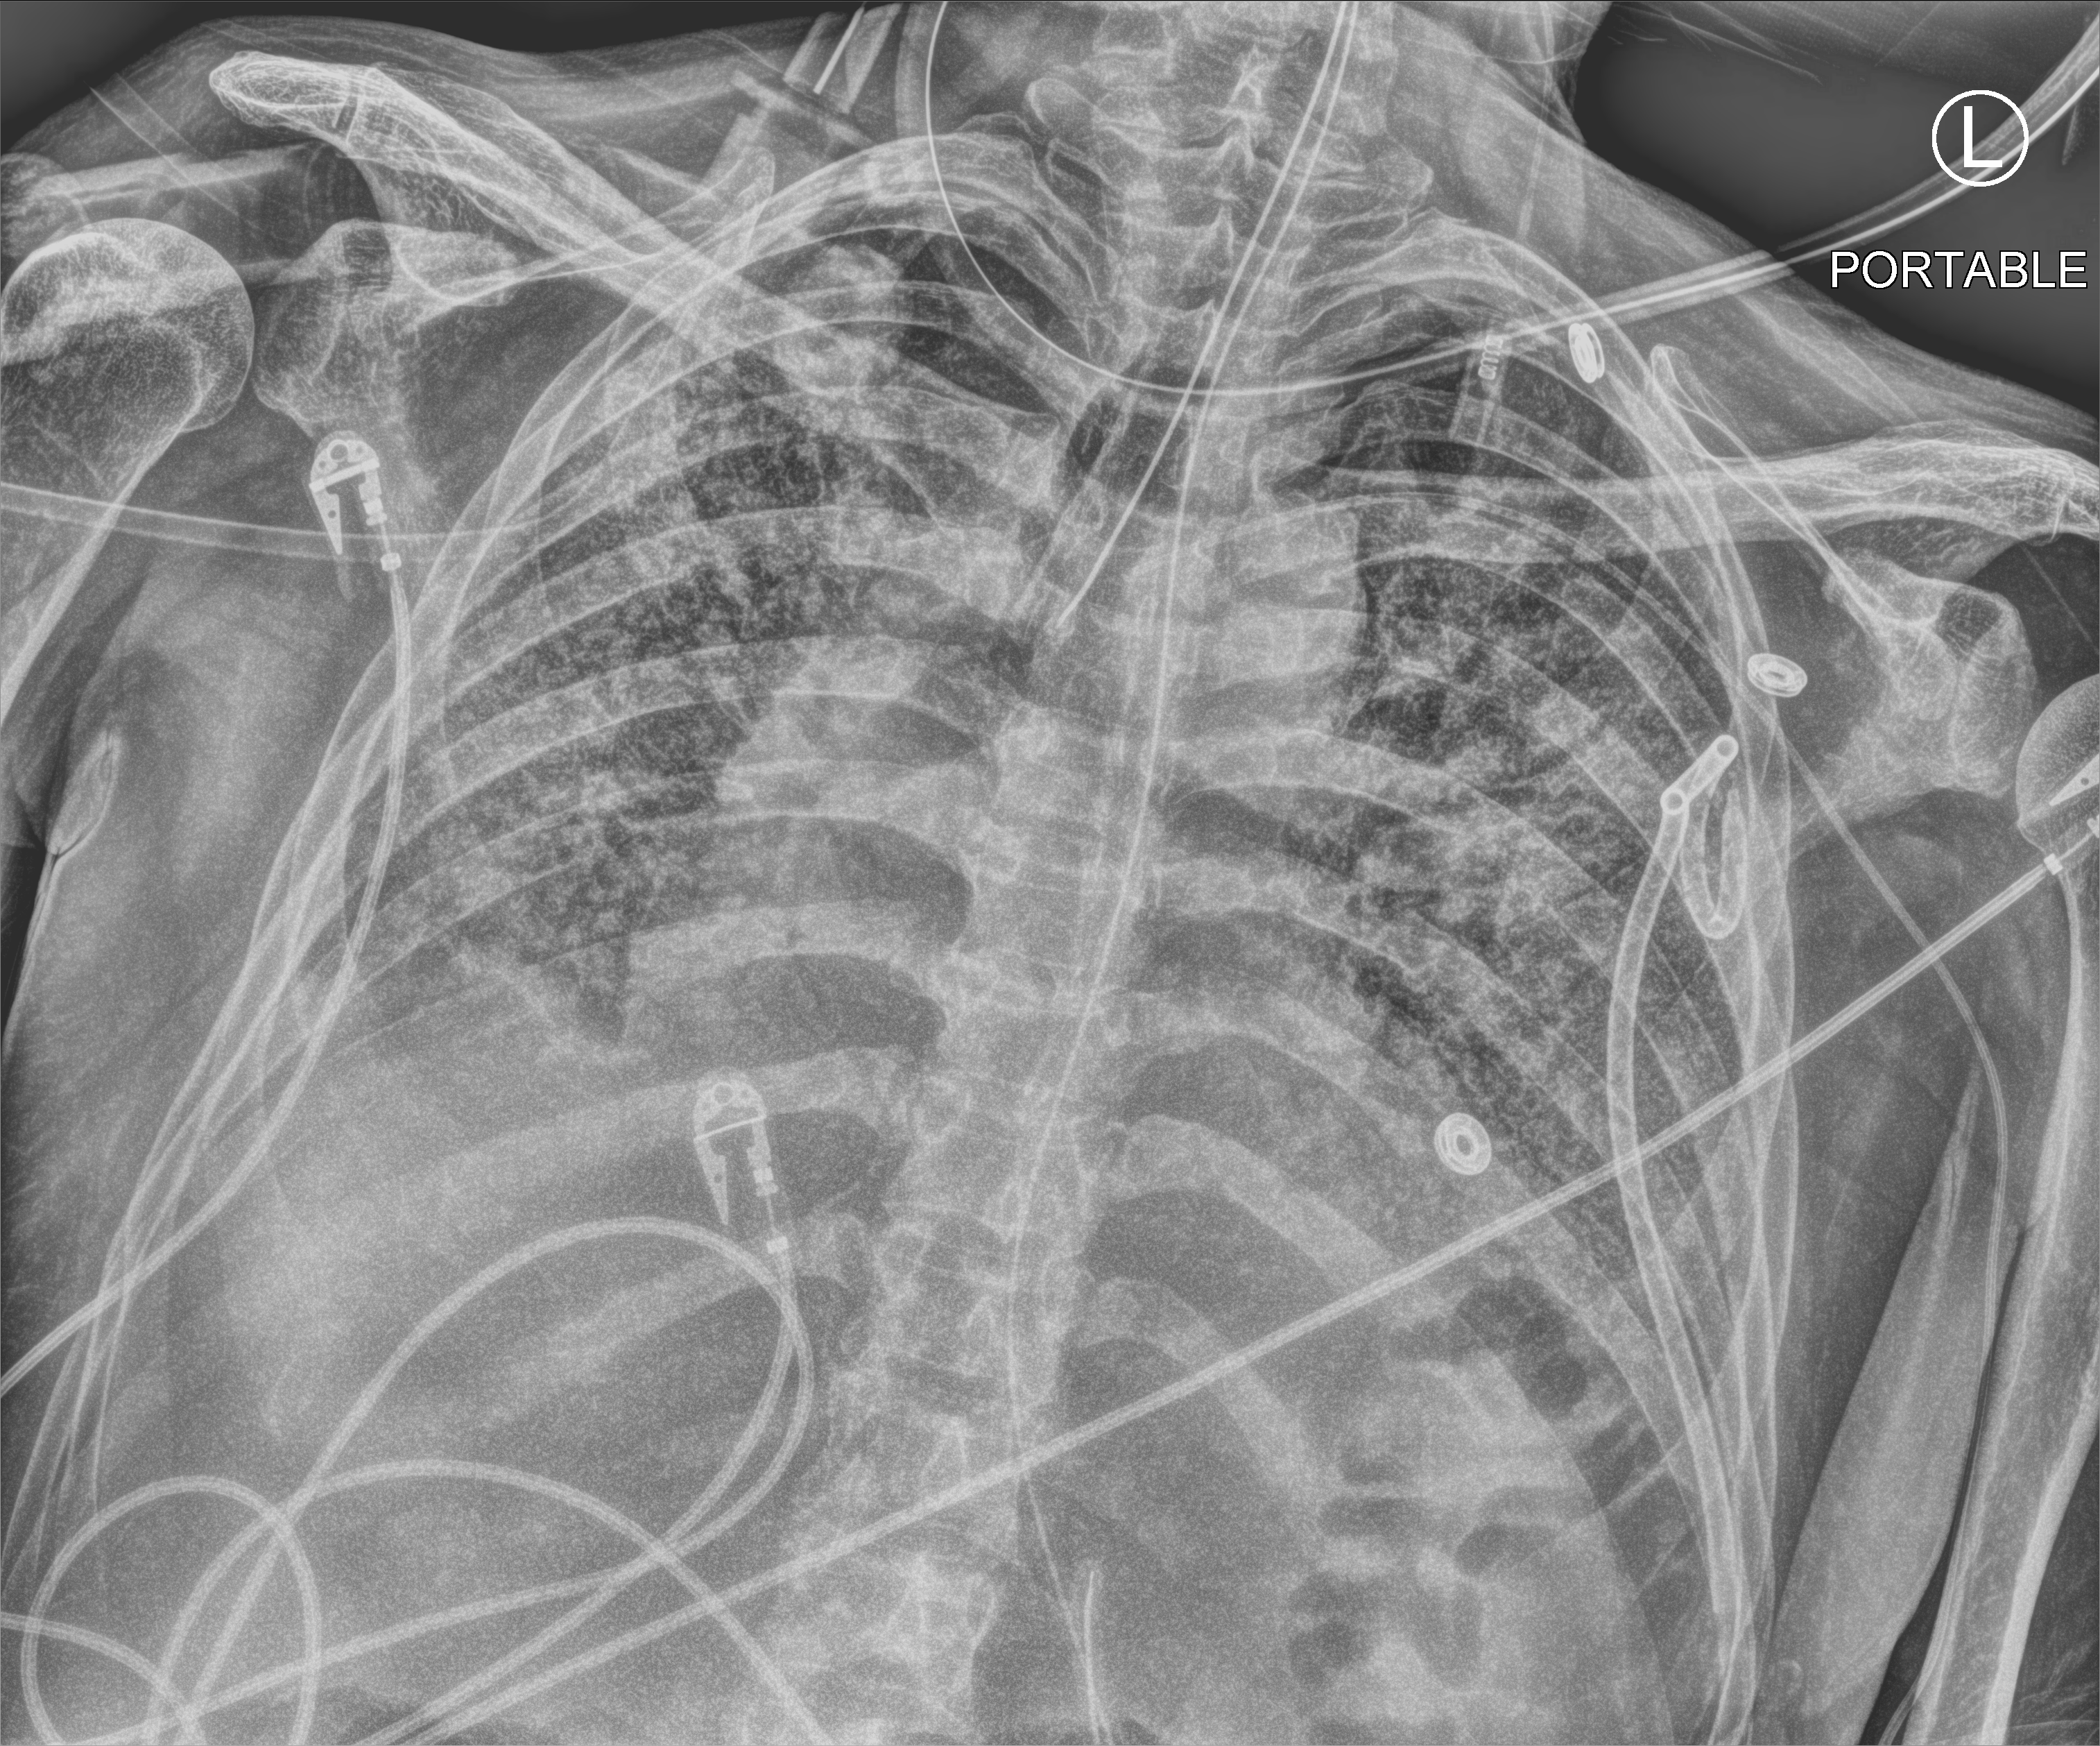
Bedside chest radiograph (computed radiography); anteroposterior (AP) projection. Patient hospitalised with COVID-19; male, aged 60–74 years.
Admission-level facts for this patient (not findings on this image; timing relative to this image not recorded): admitted to intensive care during this hospital stay: yes.